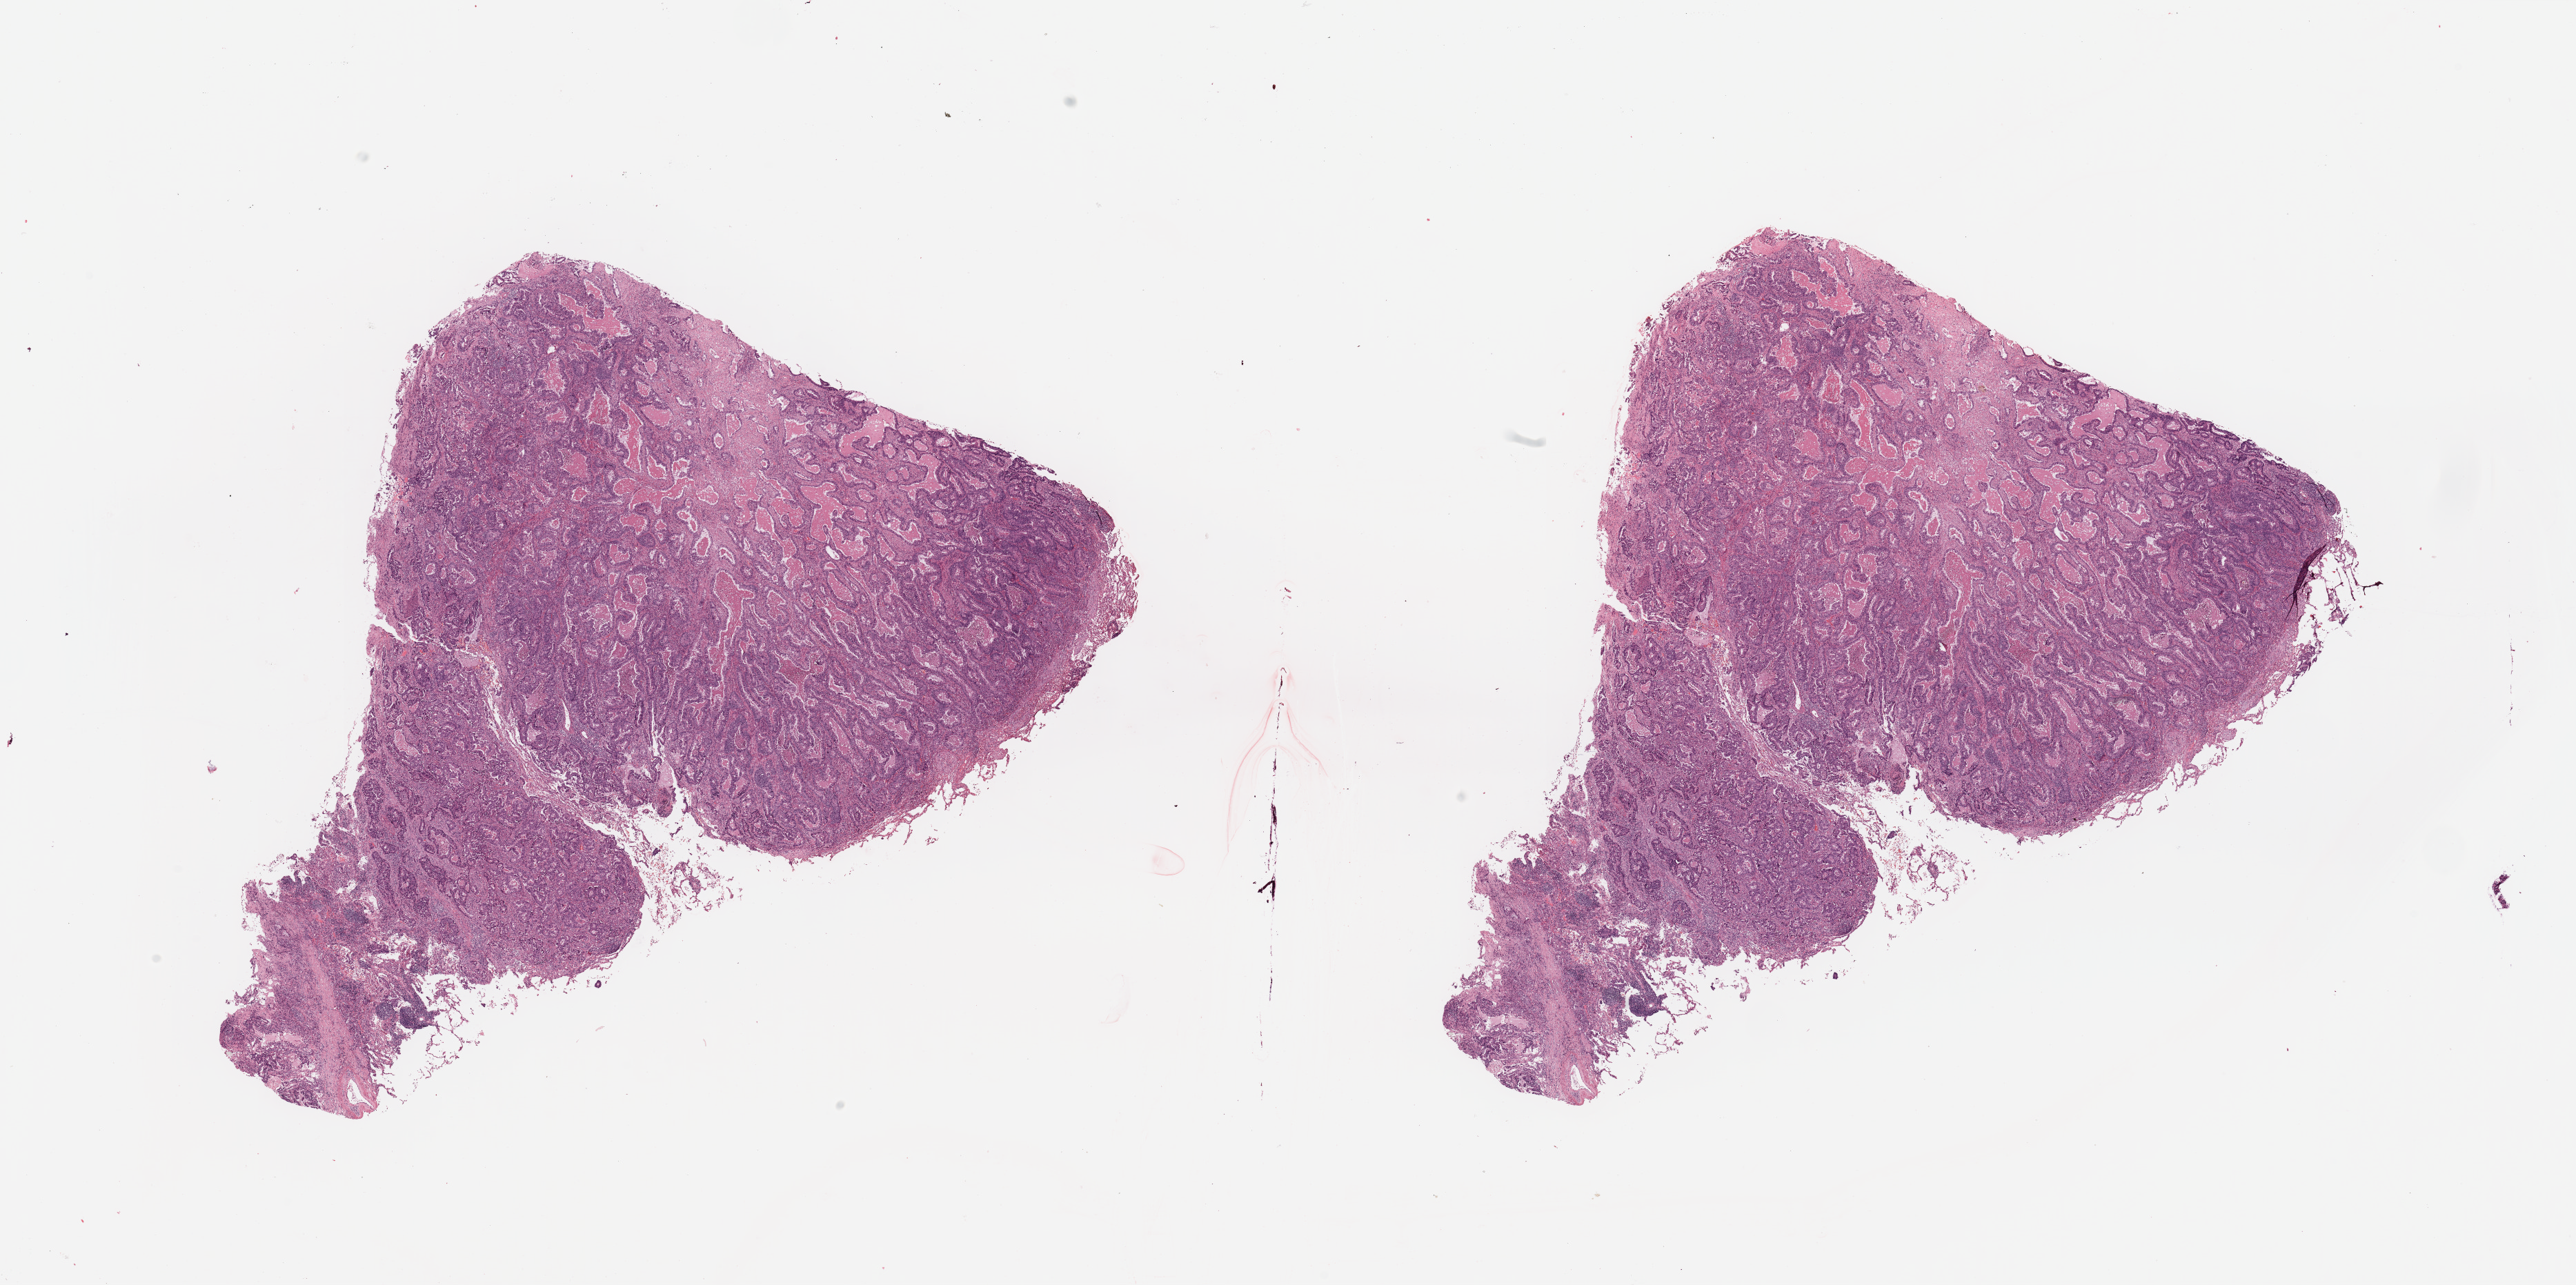
H&E-stained whole-slide image, low-resolution overview of the scanned area, about 29.5 x 14.7 mm (acquisition: 20x scan), tumour tissue sample, lung. Patient: male, age 63 years. Histologic grade: G2 (moderately differentiated).
Primary tumour site (as recorded): right middle lobe. Histologic diagnosis: Adenocarcinoma, NOS. AJCC pathologic stage: IIA.